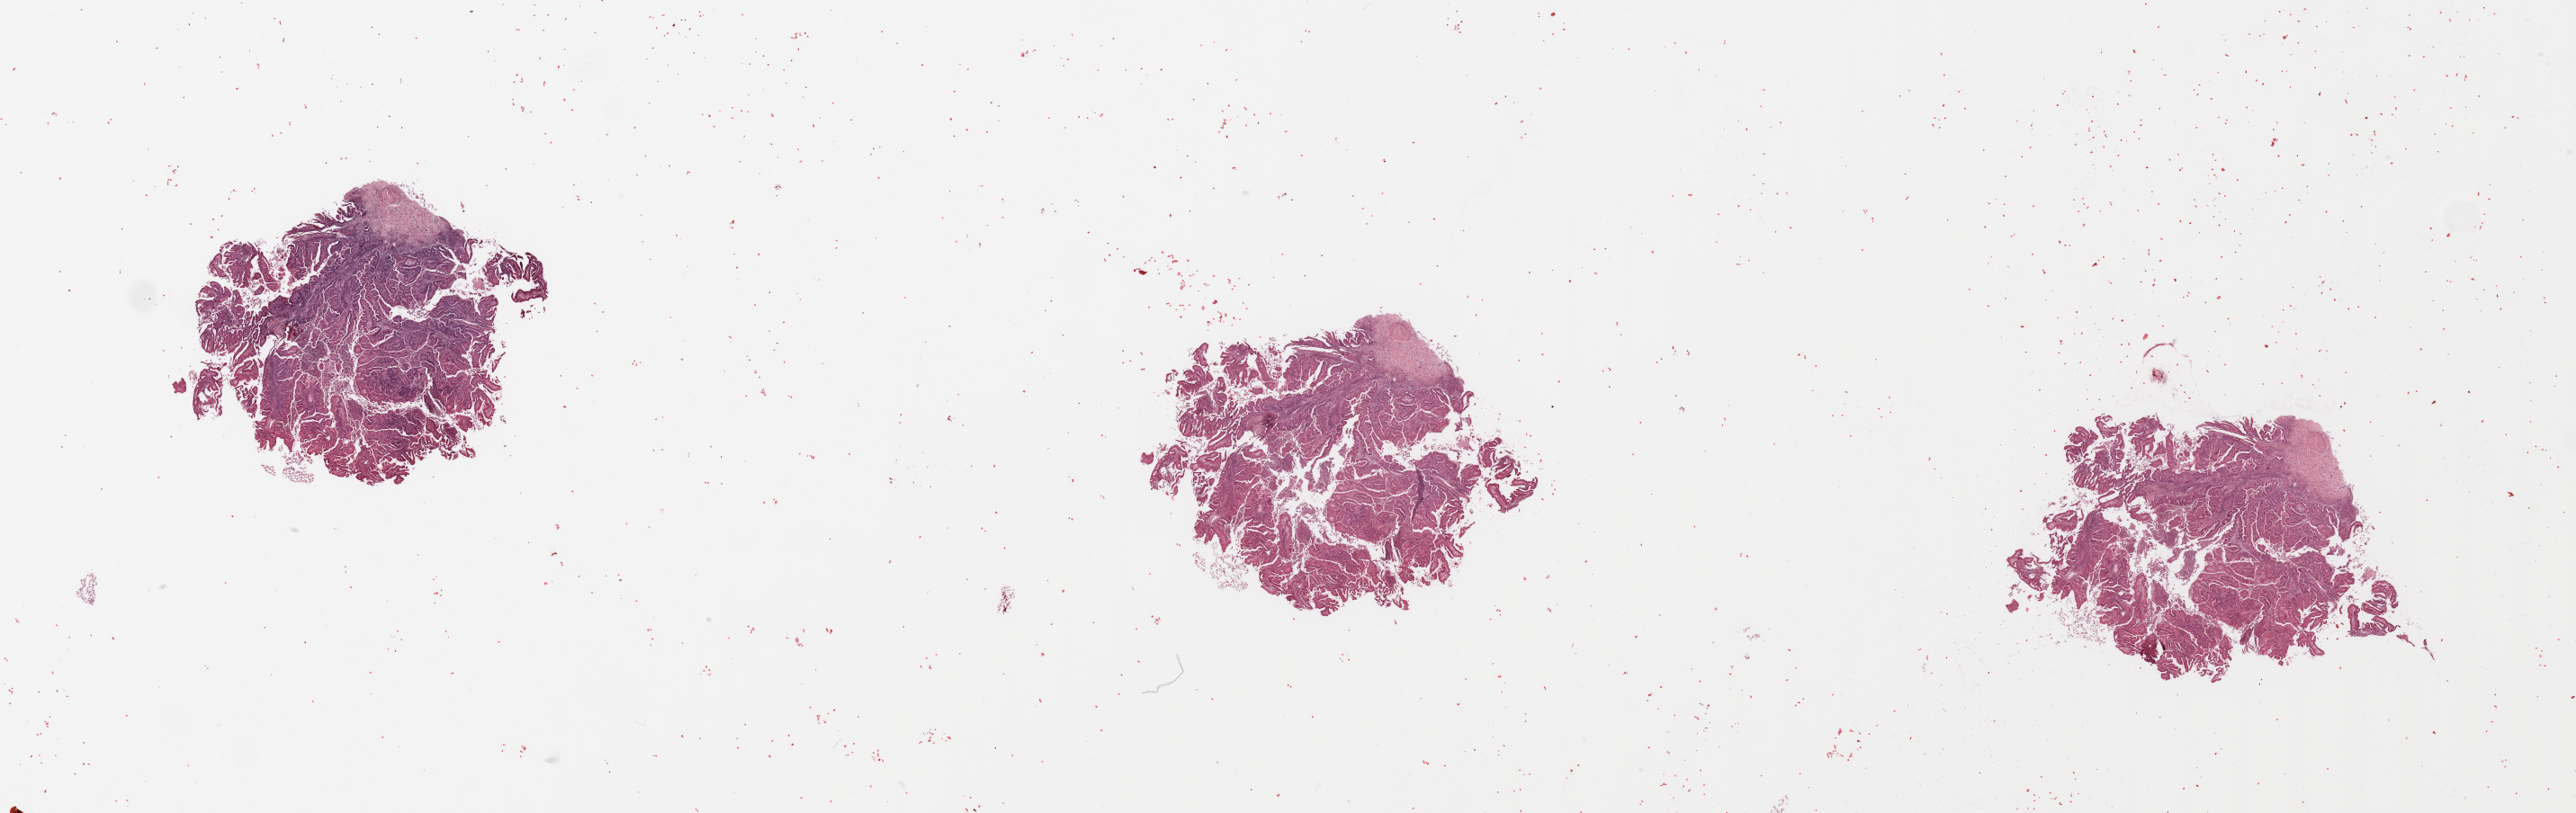
Digitized H&E-stained tissue section (whole slide), shown as a low-resolution overview of the whole scanned area (about 45.3 x 14.3 mm), uterus, tumour tissue. 59-year-old female patient. Histologic grade: G2 (moderately differentiated).
Diagnosis: Endometrioid adenocarcinoma, NOS. Primary tumour site (as recorded): anterior endometrium. AJCC pathologic stage: II.